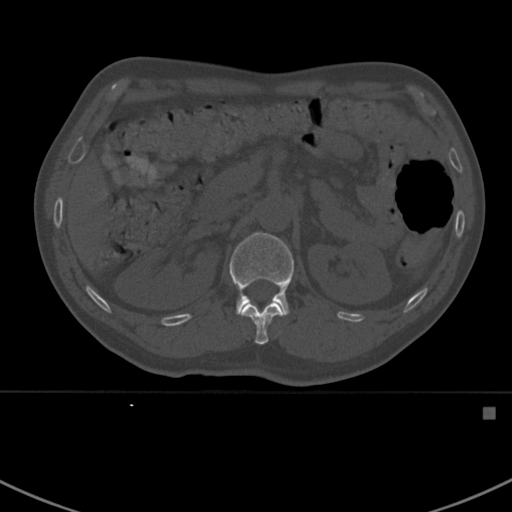
CT including the spine, one axial slice; position 318 of 412 along the scan axis; reconstruction kernel Br40s; bone window (W 1800 / L 400 HU); 1.5 mm slice thickness; 512 × 512 image matrix. Patient: male, 59 years. From the clinical record (not read from this slice): primary cancer: prostate.
Structures marked on this image (semi-automatic segmentation, software-assisted and operator-edited):
- L1 vertebra: bounding box (x1, y1, x2, y2) in pixels: (230, 232, 294, 316)
- T12 vertebra: (242, 303, 282, 345)